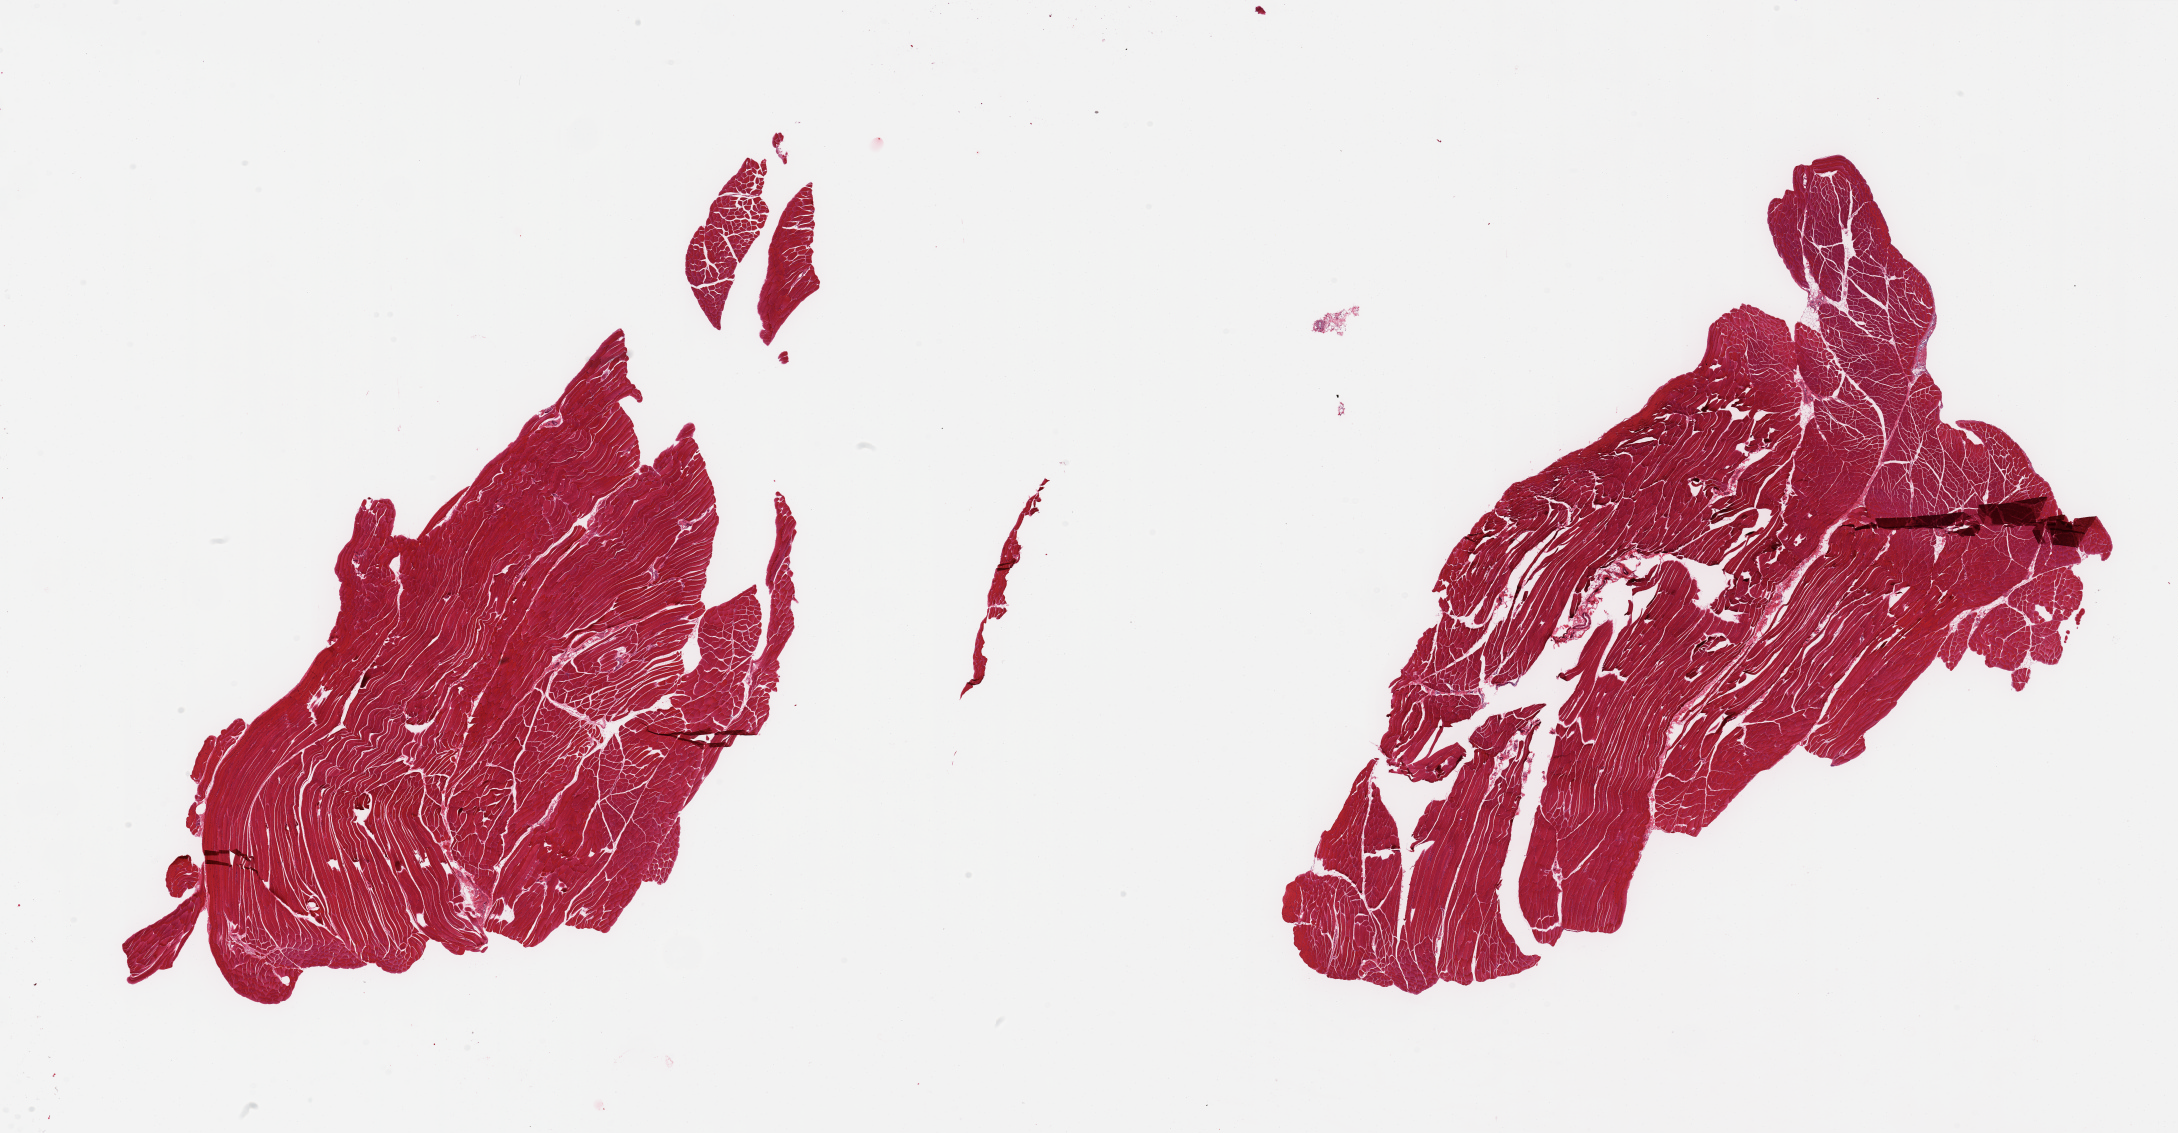
H&E whole-slide image, shown as a low-resolution overview of the whole scanned area (about 34.5 x 17.9 mm), PAXgene-fixed paraffin-embedded (PFPE) section, section of skeletal muscle (target tissue), donor tissue sample. Donor sex: male.
Reviewer comment on this tissue sample: 2 pieces.